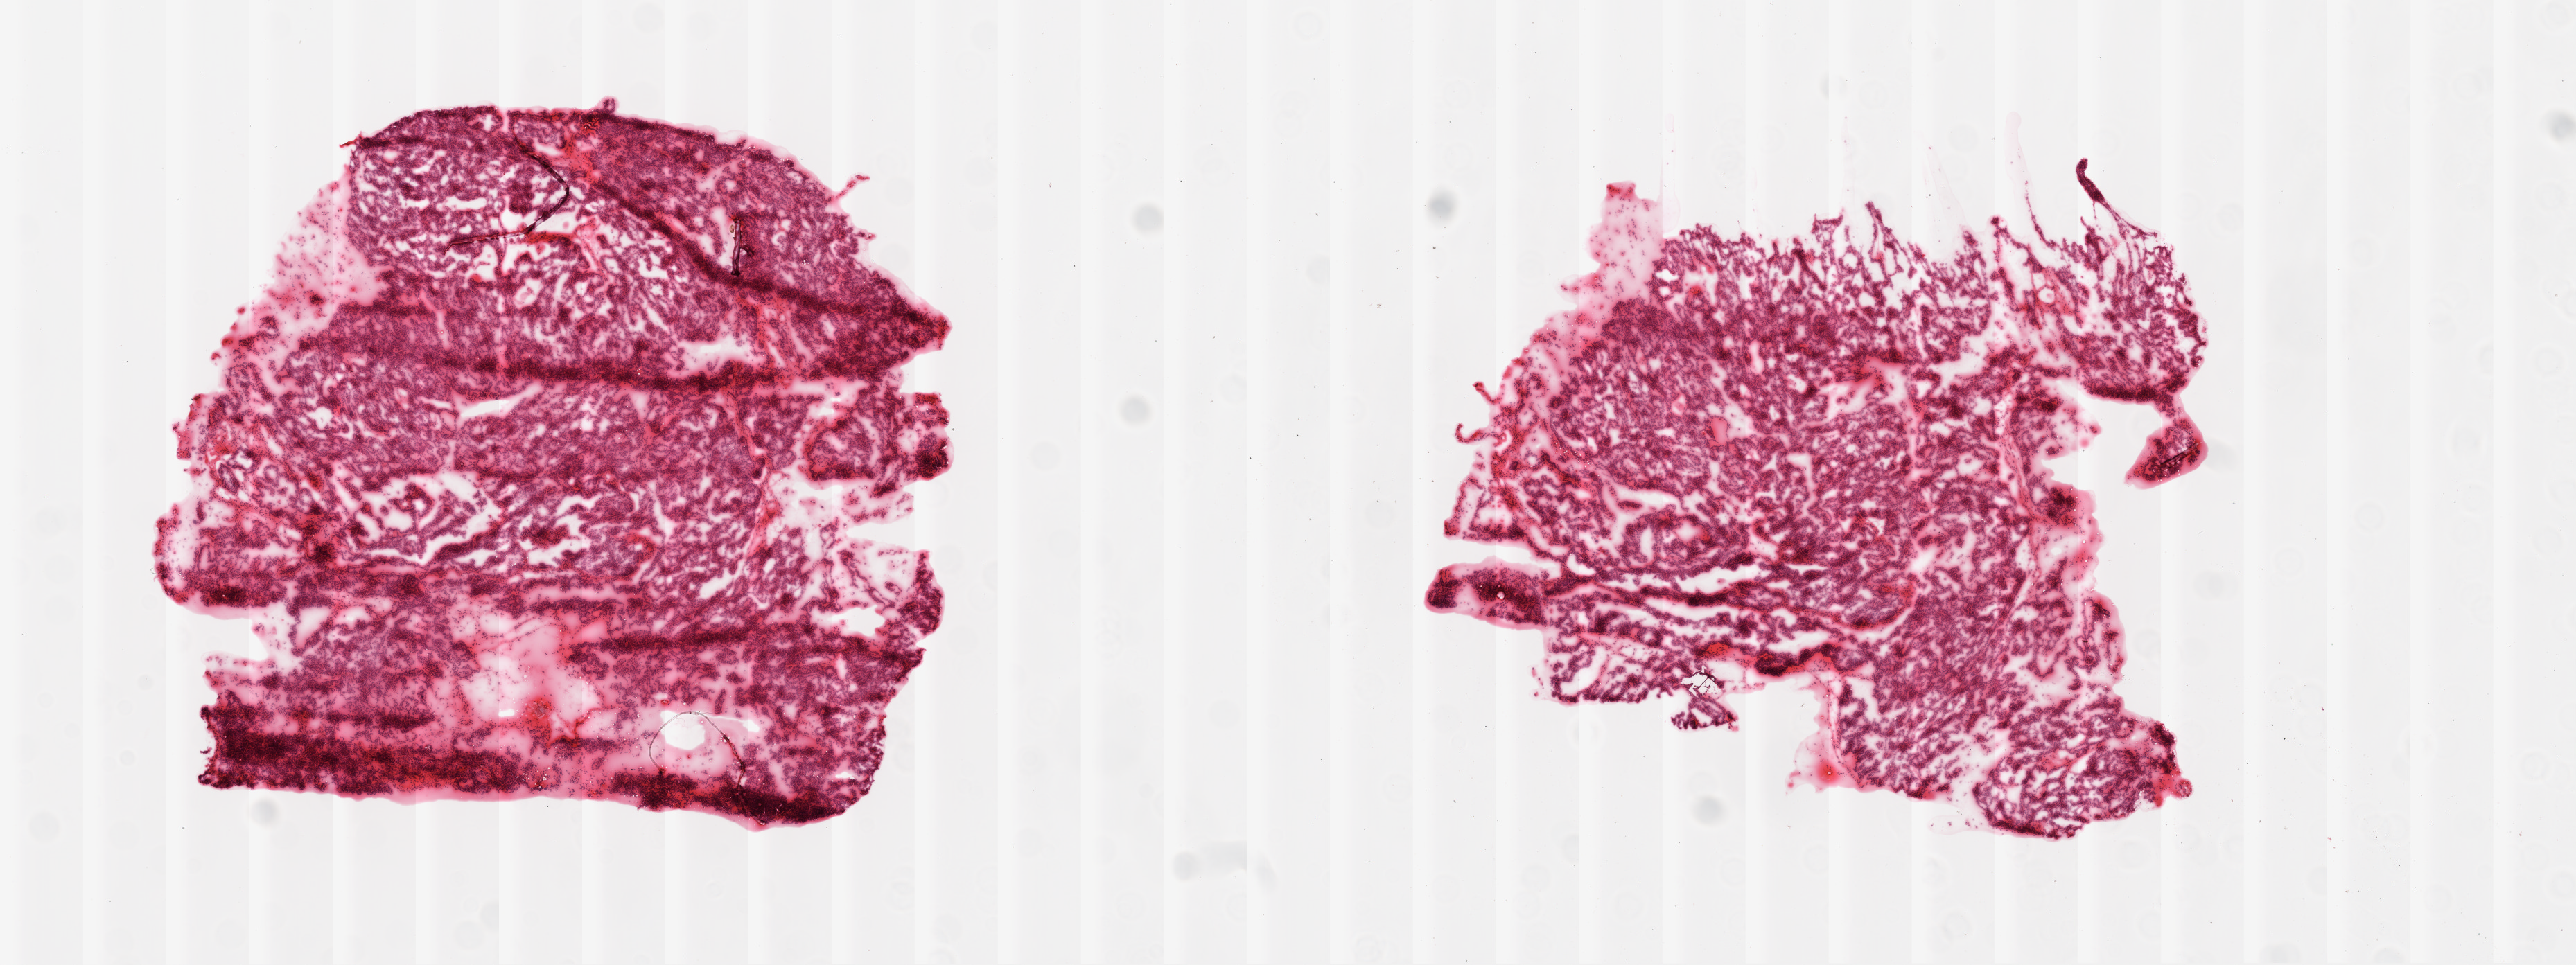
Digitized H&E tissue section (whole slide), a low-resolution overview of the entire scanned area, about 15.0 x 5.6 mm (slide scanned at 20x); frozen section from the top of the tissue portion; ovary, primary tumour sample. Female patient; age at initial diagnosis 78 years. Histologic grade: G3 (poorly differentiated). Composition of this section per pathologist review: tumour cells 95%, tumour nuclei 98%, normal cells 0%, stromal cells 5%, necrosis 0%.
- FIGO stage: IIIC
- pathologic diagnosis: Serous cystadenocarcinoma, NOS